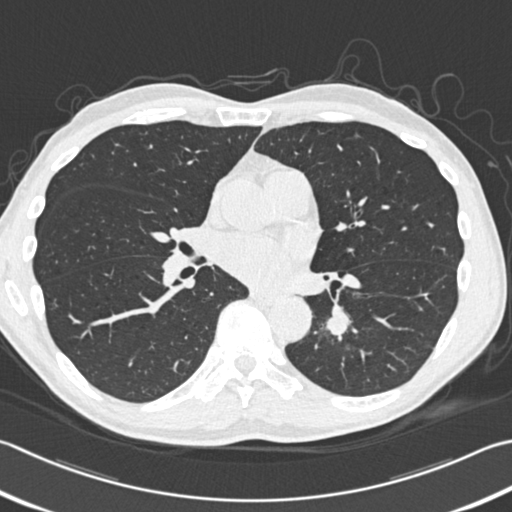
Low-dose screening chest CT, one axial slice. Slice 175 of 354 in the series (ordered by position). Reconstruction kernel B30f. Lung window (W 1500 / L -600 HU). 1 mm slice thickness. 512 × 512 image matrix, field of view 346 × 346 mm.
Annotated regions visible in this slice (expert manual segmentation):
- lesion 1 (tumor, lower lobe of left lung): bounding box [x1, y1, x2, y2] px = [326, 315, 349, 337]